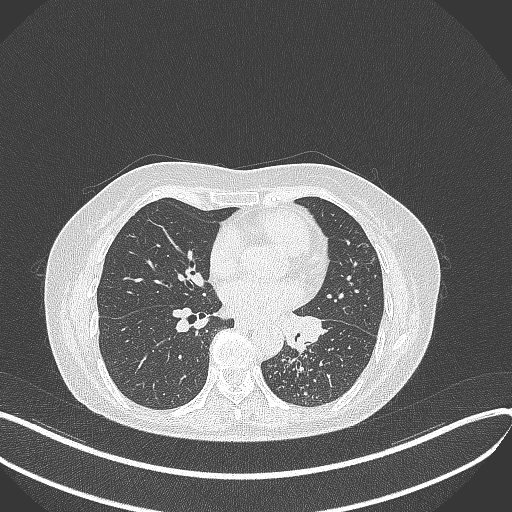
Chest CT, one axial slice. Position 192 of 429 along the scan axis. Reconstruction kernel B70f. 100 kVp. Lung window (W 1500 / L -600 HU). 512 × 512 image matrix, field of view 400 × 400 mm. Patient: female, 63 years. Case-level facts recorded for this patient, not image findings: clinical TNM (as recorded): T1b N0 M0.
Annotated regions visible in this slice (bounding box drawn by a radiologist):
- lung tumour (recorded histology: adenocarcinoma): box from (x=279, y=309) to (x=323, y=352) px